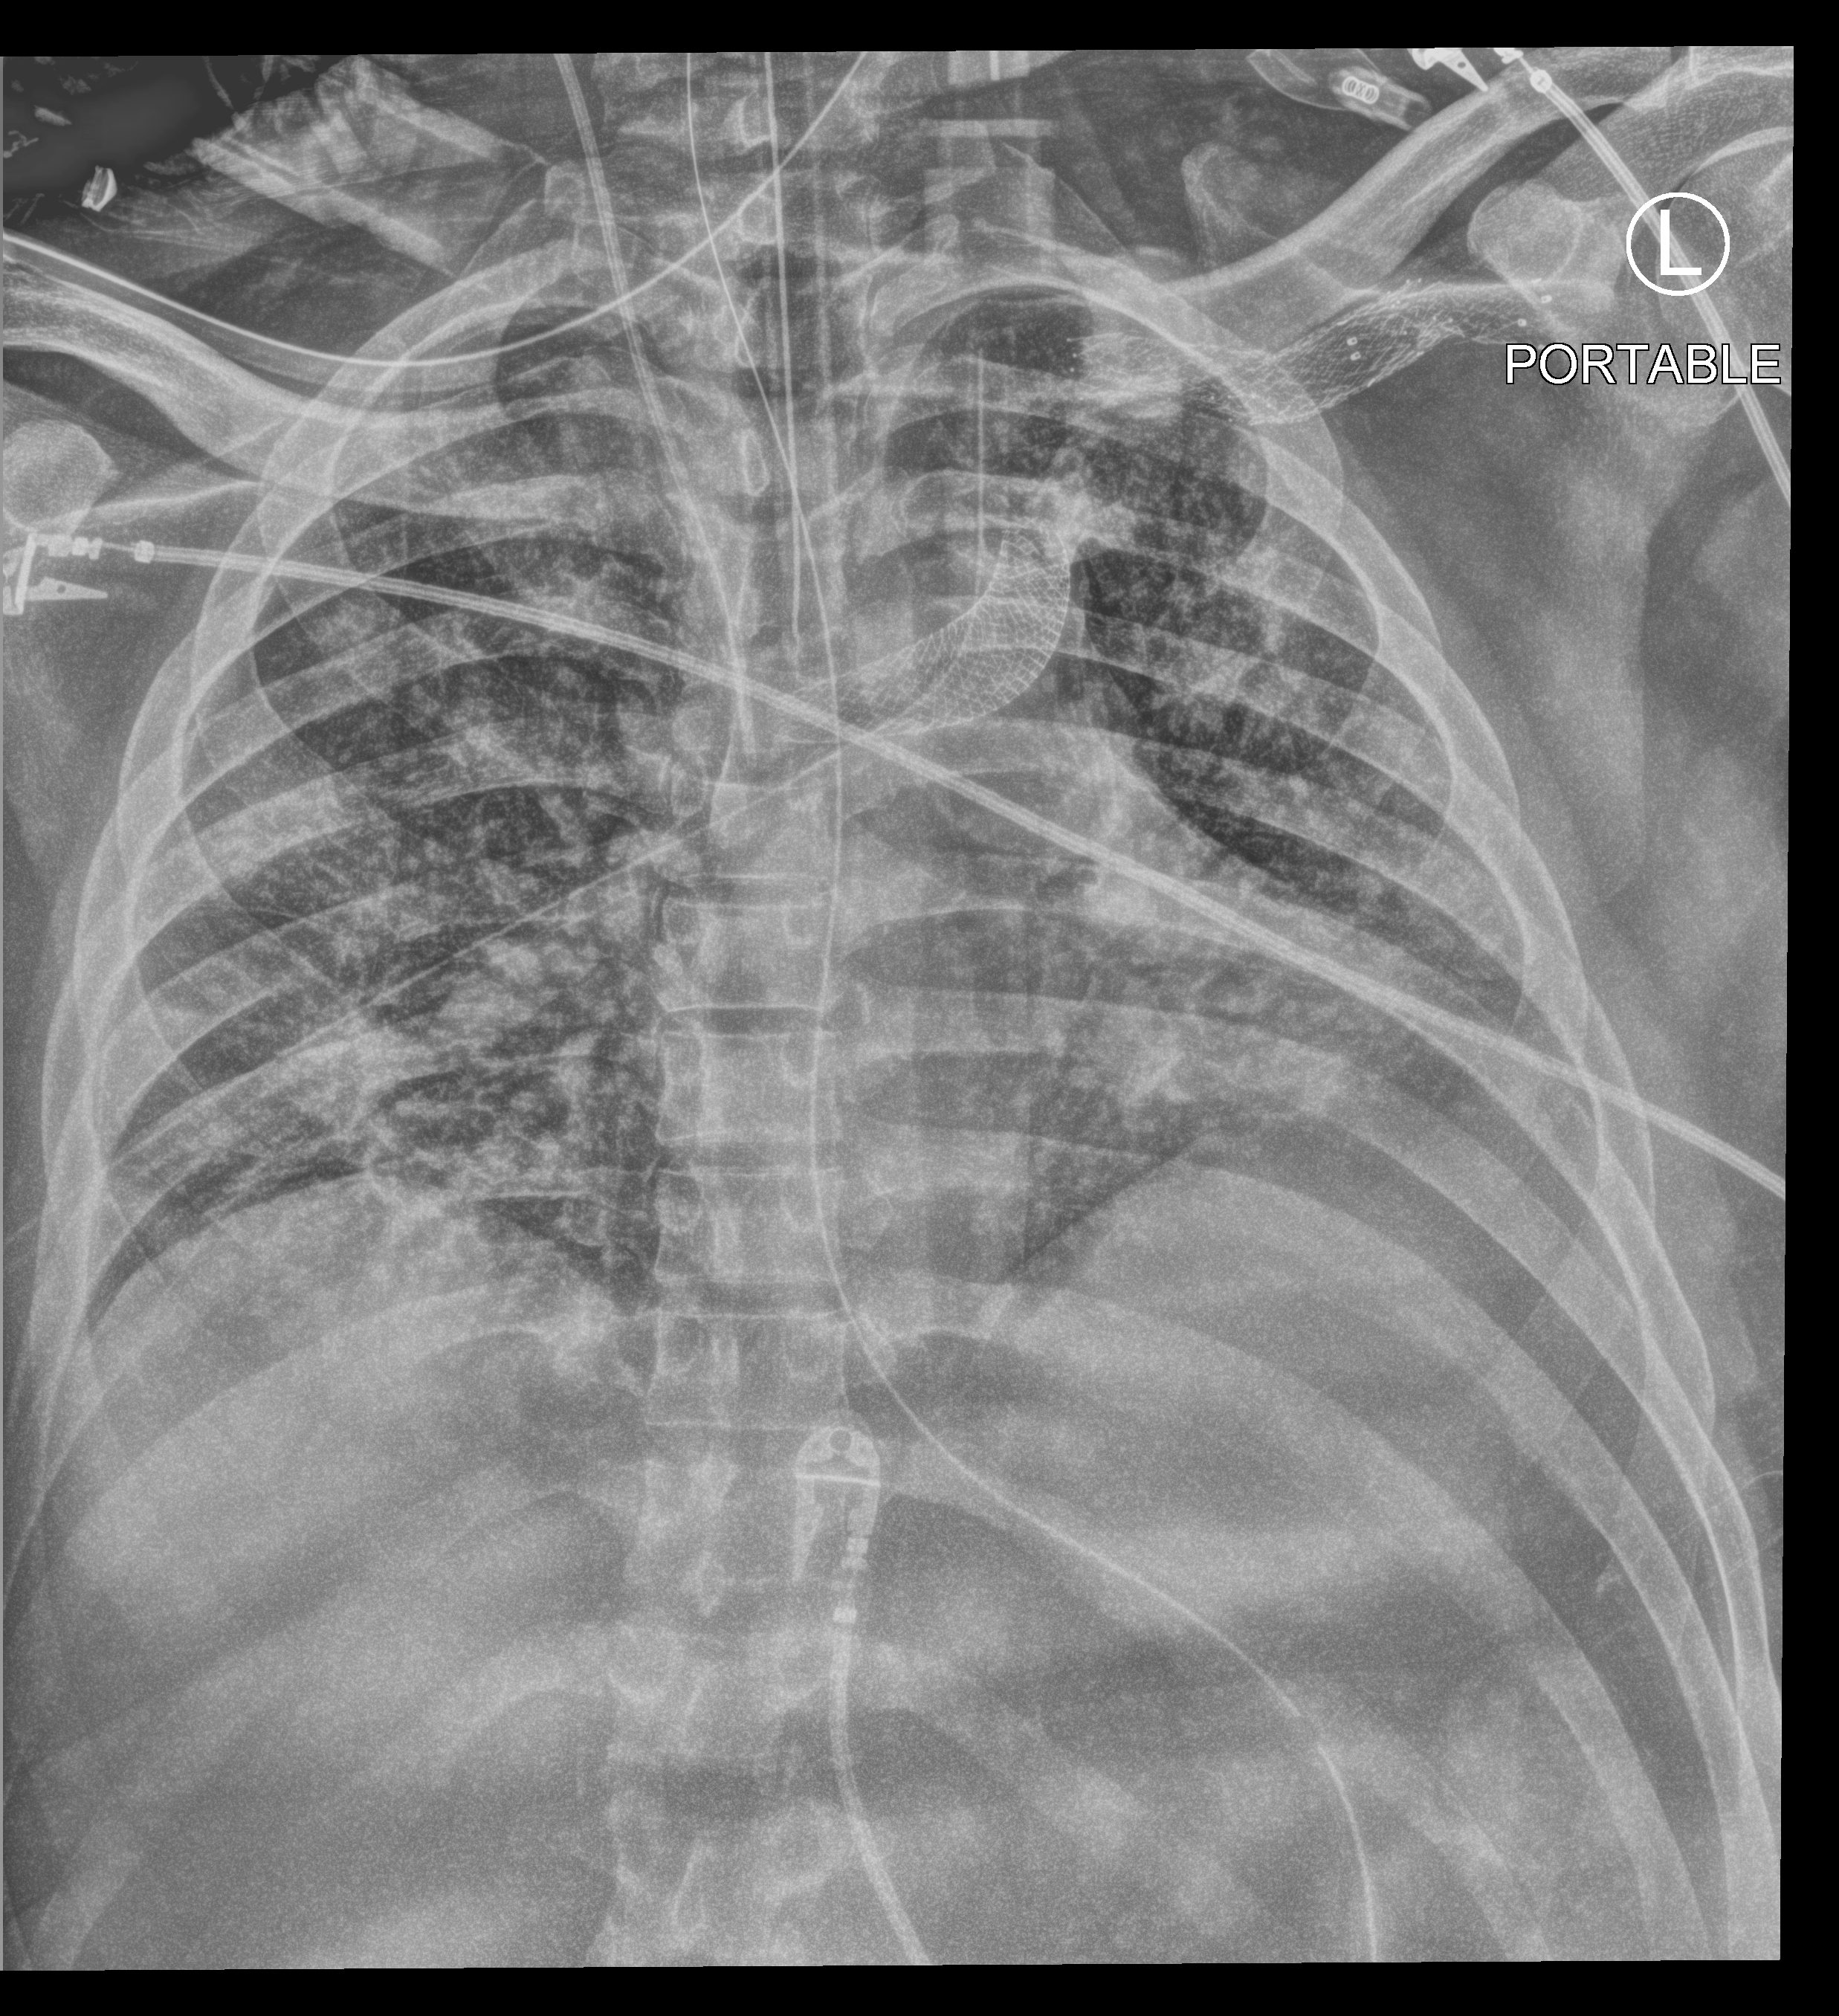
Chest X-ray (portable). Male patient hospitalised with COVID-19, age 18–59 years.
Admission-level facts for this patient (not findings on this image; timing relative to this image not recorded): length of hospital stay: 41 days.